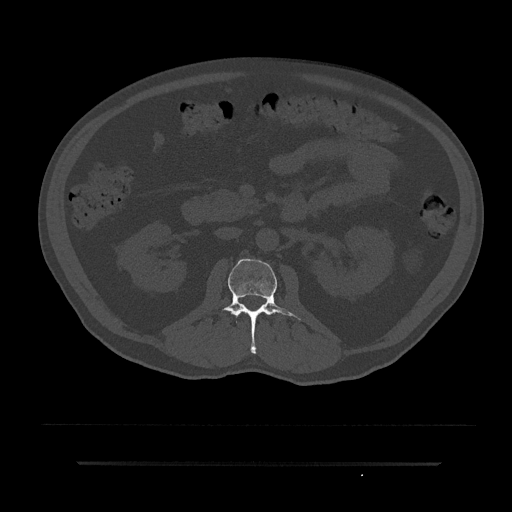
CT including the spine, one axial slice; position 76 of 797 along the scan axis; bone window (W 1800 / L 400 HU); 0.5 mm slice thickness; 512 × 512 image matrix. Male patient, age 59 years. From the clinical record (not read from this slice): primary cancer: bile ducts; vertebrae with lytic lesions (as recorded): T10.
Outlined on this slice (semi-automatically segmented with operator editing):
- L1 vertebra: bounding box [x1, y1, x2, y2] px = [240, 311, 242, 313]
- L2 vertebra: [221, 258, 302, 354]